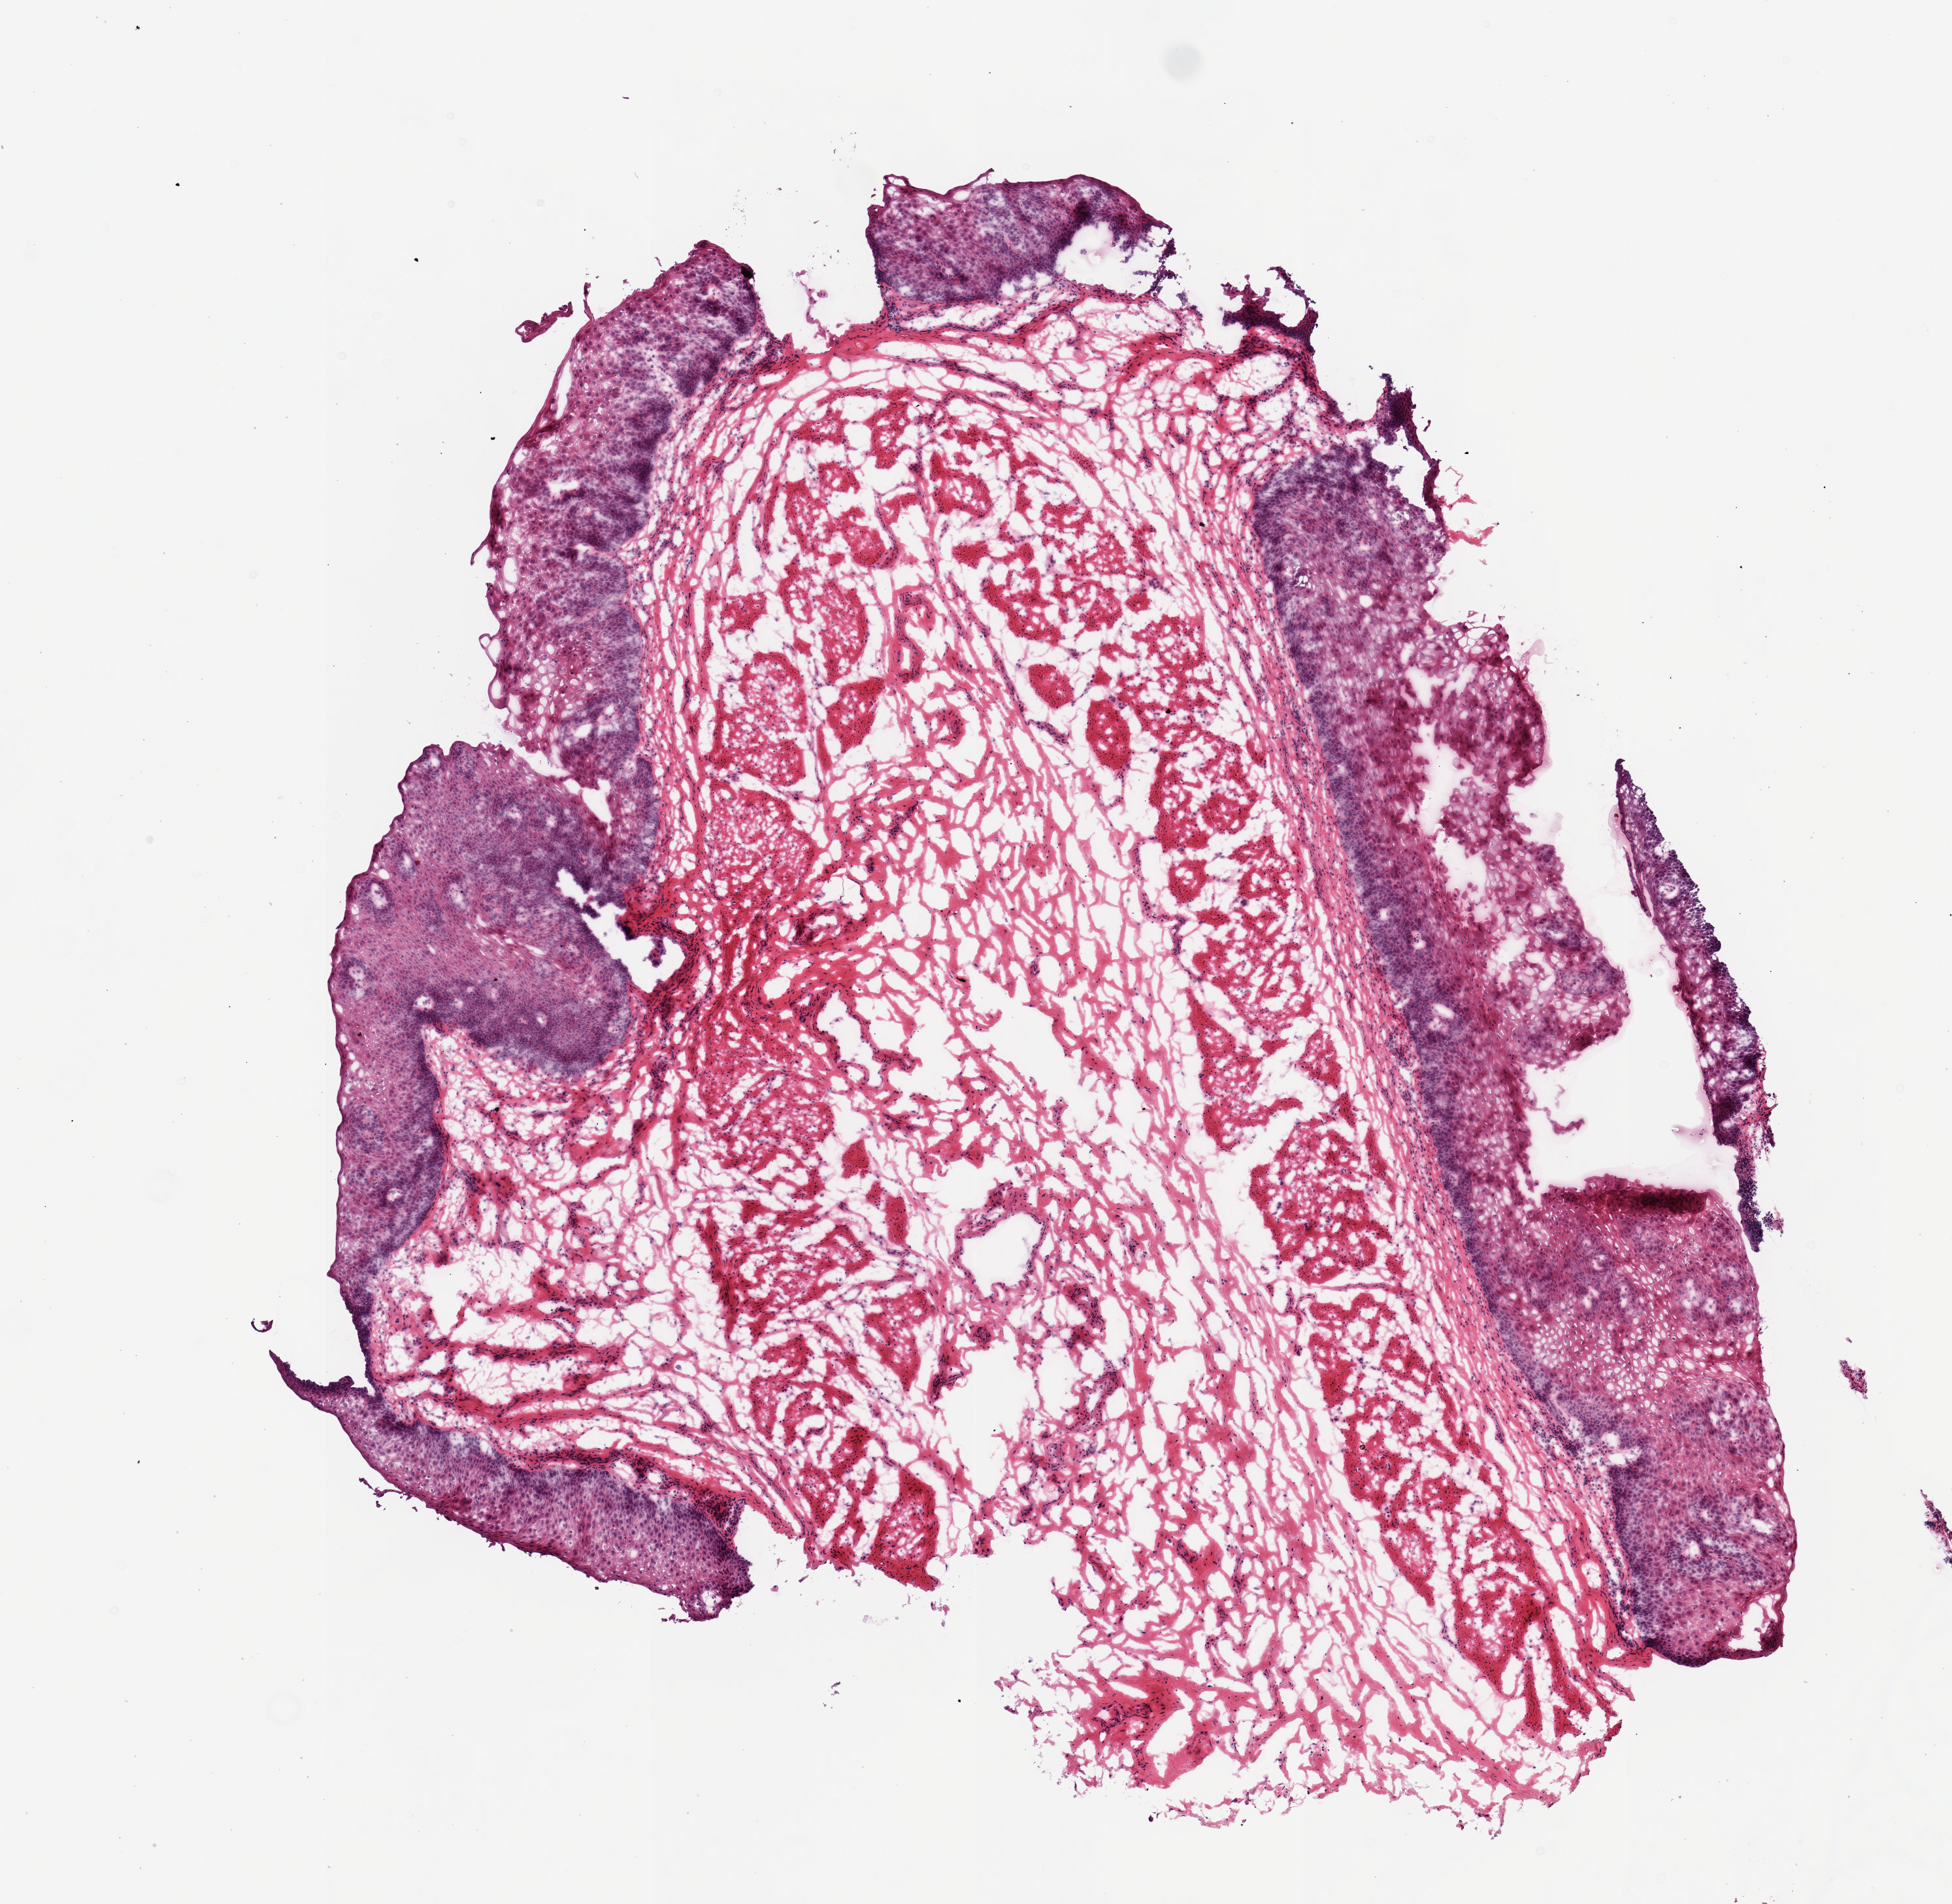
Digitized hematoxylin and eosin (H&E)-stained section — shown as a low-resolution overview of the whole scanned area (about 5.9 x 5.8 mm), frozen section, sampled site (target tissue): esophageal mucous membrane, donor tissue sample. Donor sex: male.
Pathologist's review note for this sample: 1 piece.